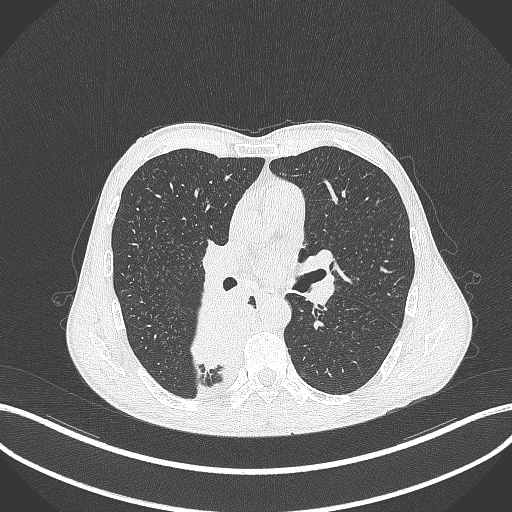
Chest CT, one axial slice; position 210 of 371 along the scan axis; 120 kVp; lung window (W 1500 / L -600 HU); 1 mm slice thickness; 512 × 512 image matrix, field of view 400 × 400 mm. Patient: male, 58 years. From the clinical record (not read from this slice): clinical TNM (as recorded): T3 N1 M1.
Outlined on this slice (bounding box drawn by a radiologist):
- lung tumour (recorded histology: squamous cell carcinoma): bounding box <186,285,260,376> (left, top, right, bottom; pixels)